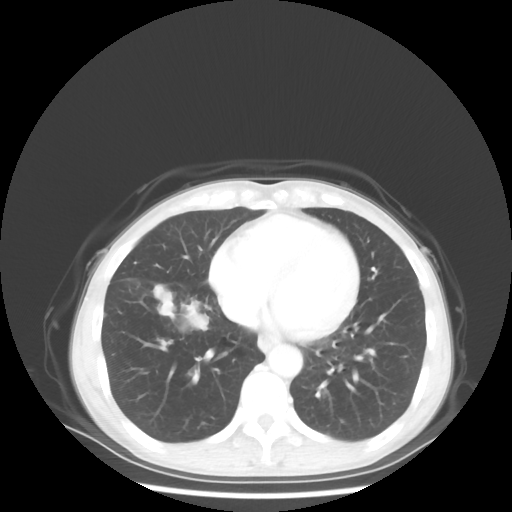
Chest CT, one axial slice. Position 19 of 56 along the scan axis. Reconstruction kernel STANDARD. Lung window (W 1500 / L -600 HU). 512 × 512 image matrix, field of view 360 × 360 mm. Female patient, age 57 years. From the clinical record (not read from this slice): clinical TNM (as recorded): T1c N3 M1a; histopathological grade: G3.
Annotated regions visible in this slice (rectangle marked by the reading radiologist):
- lung tumour (recorded histology: adenocarcinoma): box from (x=175, y=303) to (x=211, y=336) px